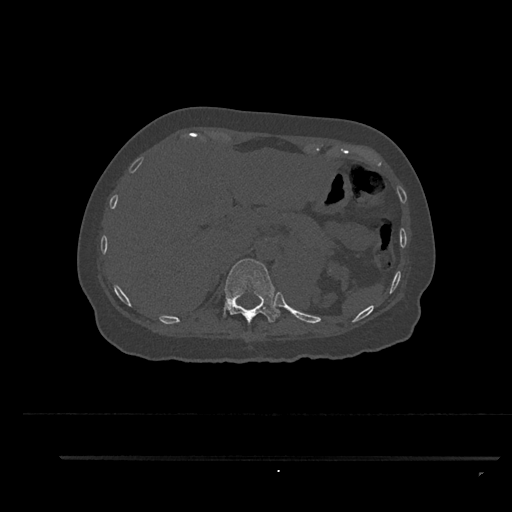
CT including the spine, one axial slice. Slice 317 of 797 in the series (ordered by position). Bone window (W 1800 / L 400 HU). 0.5 mm slice thickness. 512 × 512 image matrix, field of view 408 × 408 mm. Female patient, age 44 years. Case-level facts recorded for this patient, not image findings: primary cancer: renal.
Structures marked on this image (semi-automatically segmented with operator editing):
- T11 vertebra: bounding box <223,259,280,324> (left, top, right, bottom; pixels)